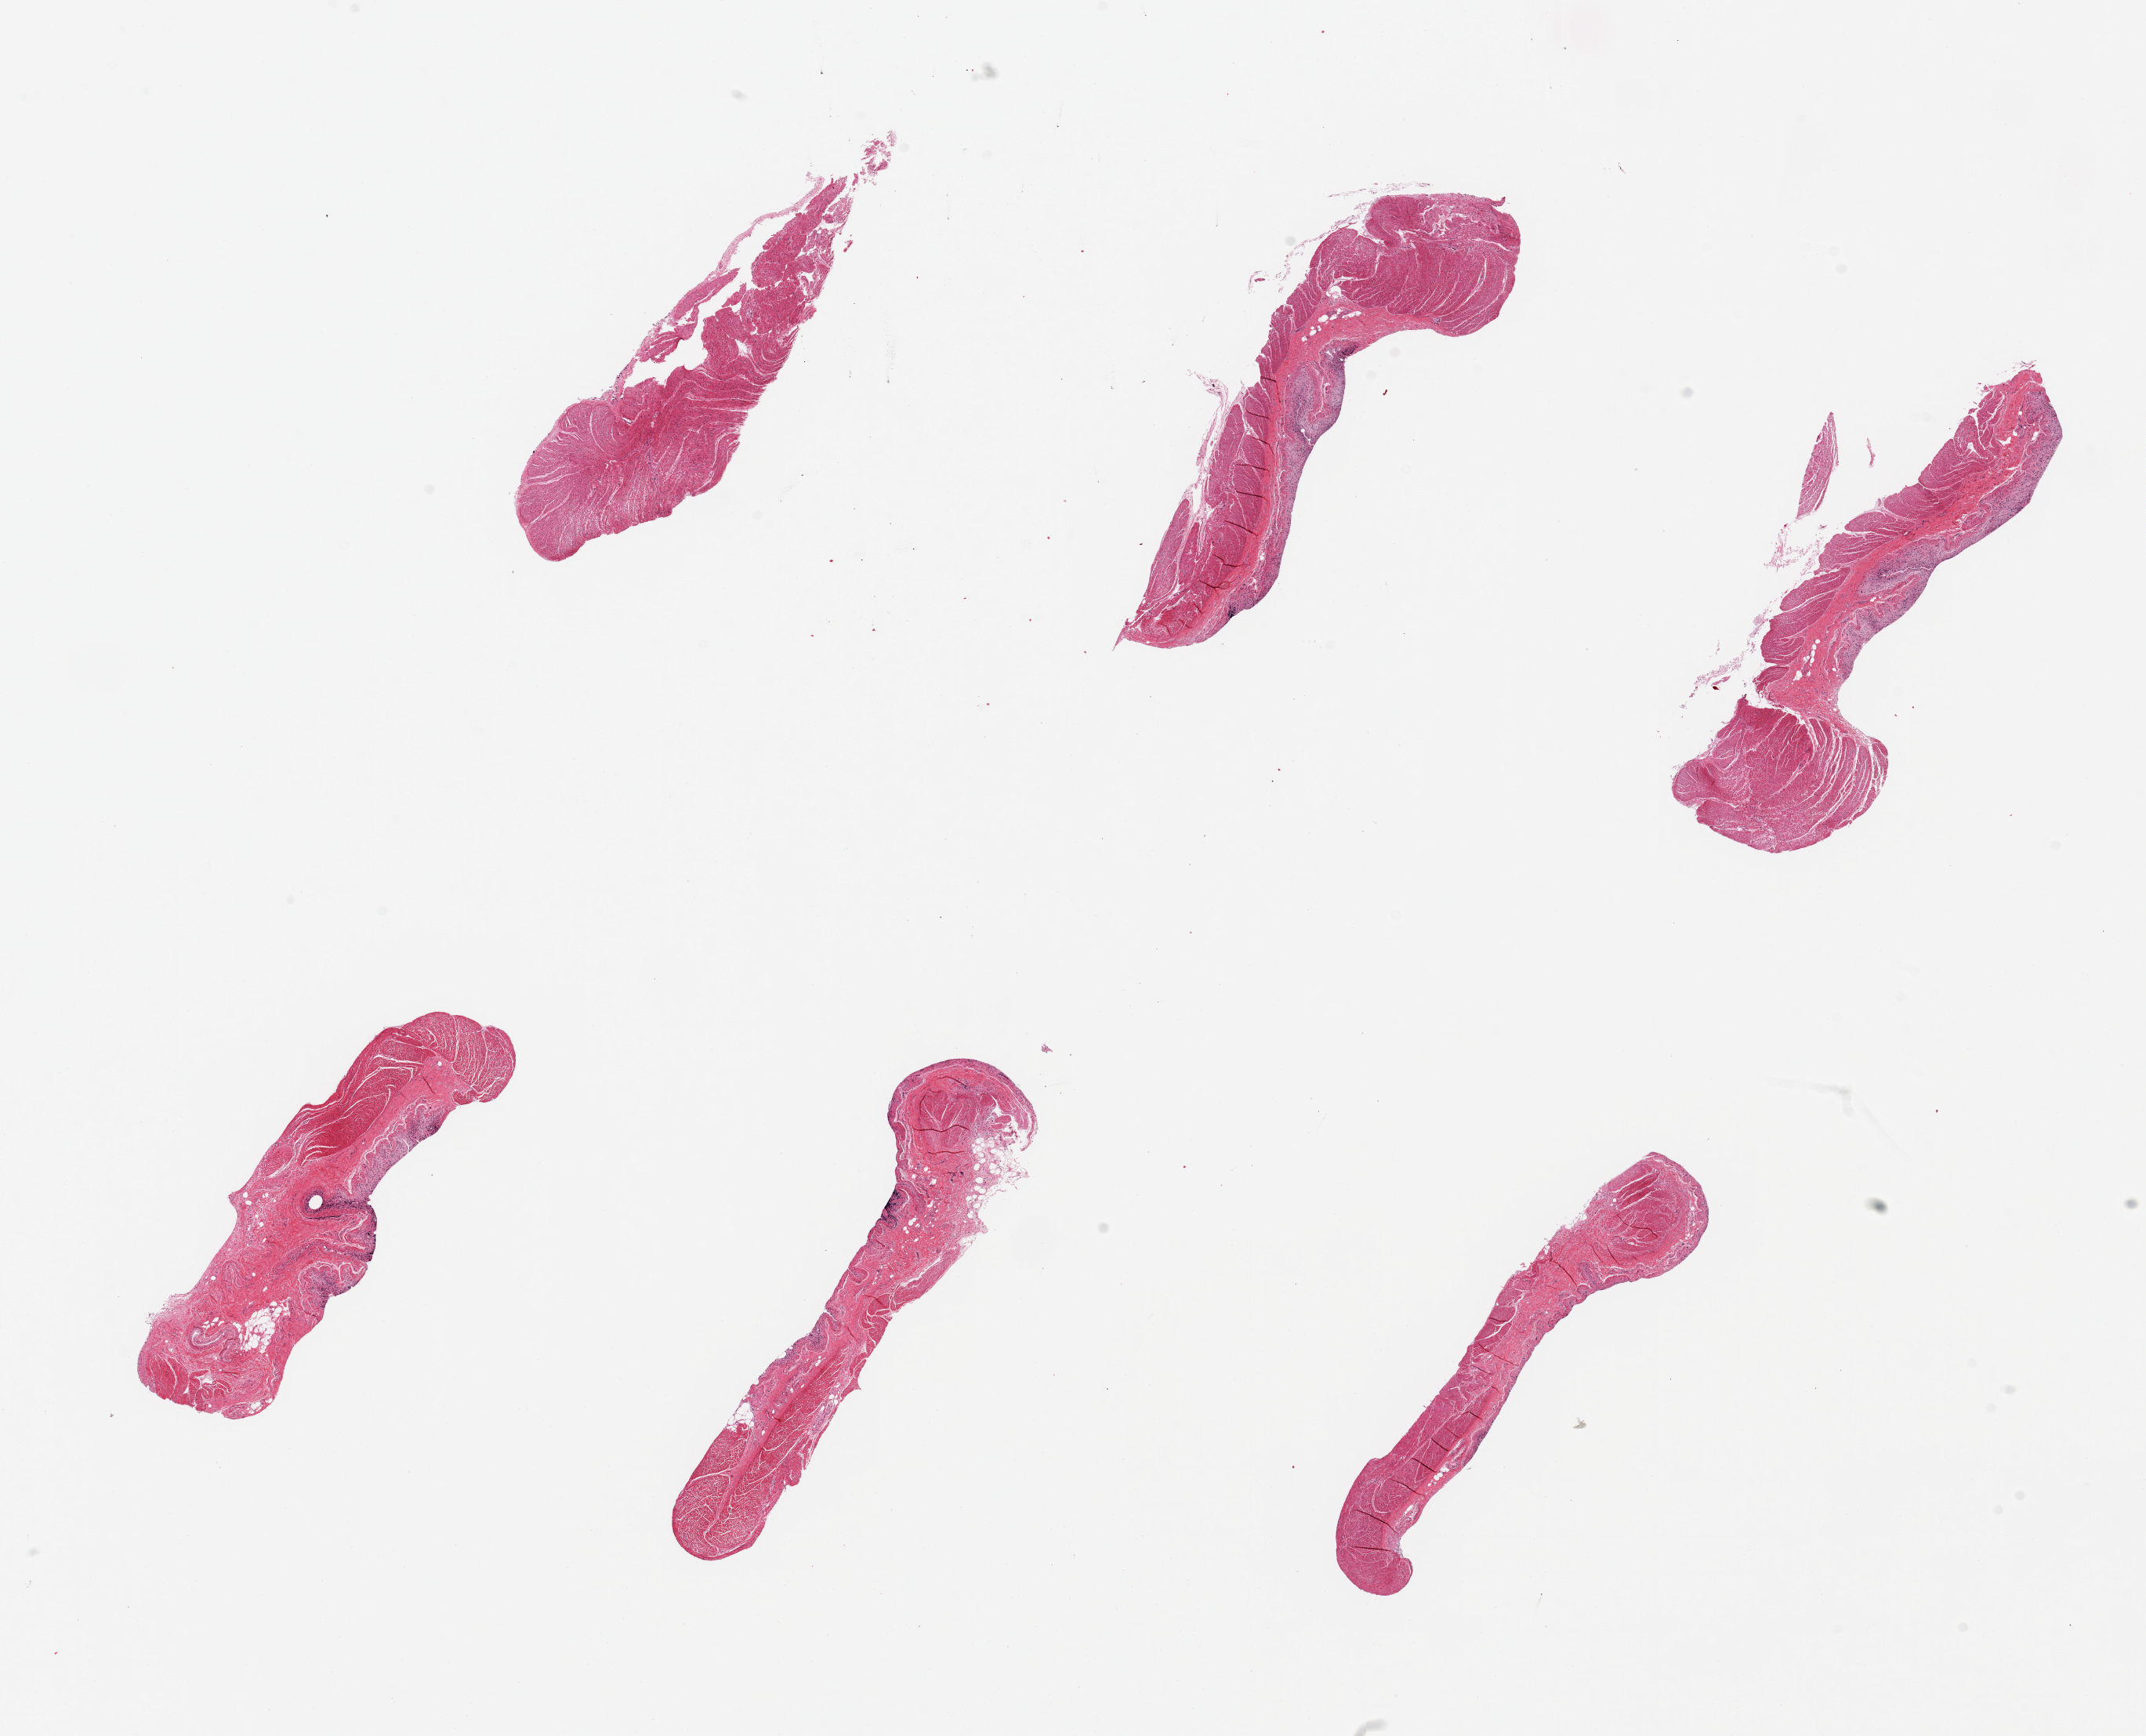
Hematoxylin and eosin (H&E) whole-slide image, brightfield, low-resolution overview of the scanned area, about 21.7 x 17.5 mm (acquisition: 20x scan). PAXgene-fixed, paraffin-embedded tissue. Section of sigmoid colon (target tissue). Donor tissue sample. Female donor.
• review note (as recorded): 6 pieces, up to 6x2mm; all muscle, no mucosa (good)